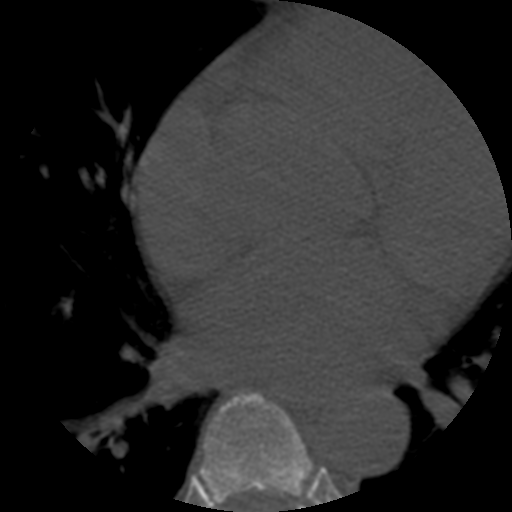
CT including the spine, one axial slice. Position 346 of 508 along the scan axis. Reconstruction kernel STANDARD. Bone window (W 1800 / L 400 HU). 1.25 mm slice thickness. 512 × 512 image matrix. Patient age 57 years. Case-level facts recorded for this patient, not image findings: primary cancer: prostate.
Annotated regions visible in this slice (semi-automatically segmented with operator editing):
- T6 vertebra: bounding box [x1, y1, x2, y2] px = [196, 392, 313, 509]
- T7 vertebra: [297, 504, 301, 506]